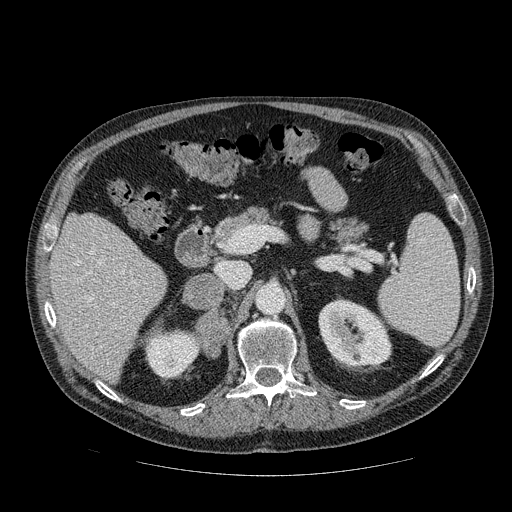
Contrast-enhanced abdominal CT, one axial slice; position 50 of 111 along the scan axis; reconstruction kernel STANDARD; intravenous contrast given; soft-tissue window (W 400 / L 40 HU); 512 × 512 image matrix, field of view 420 × 420 mm. Patient: male, 56 years. Case-level facts recorded for this patient, not image findings: diagnosis: adrenocortical carcinoma; tumour side: right adrenal; tumour size at pathology: 9 cm; Ki-67 index: 48 %; stage (as recorded): 4.
Annotated regions visible in this slice (semi-automatically segmented with operator editing):
- mass: box from (x=183, y=273) to (x=228, y=356) px